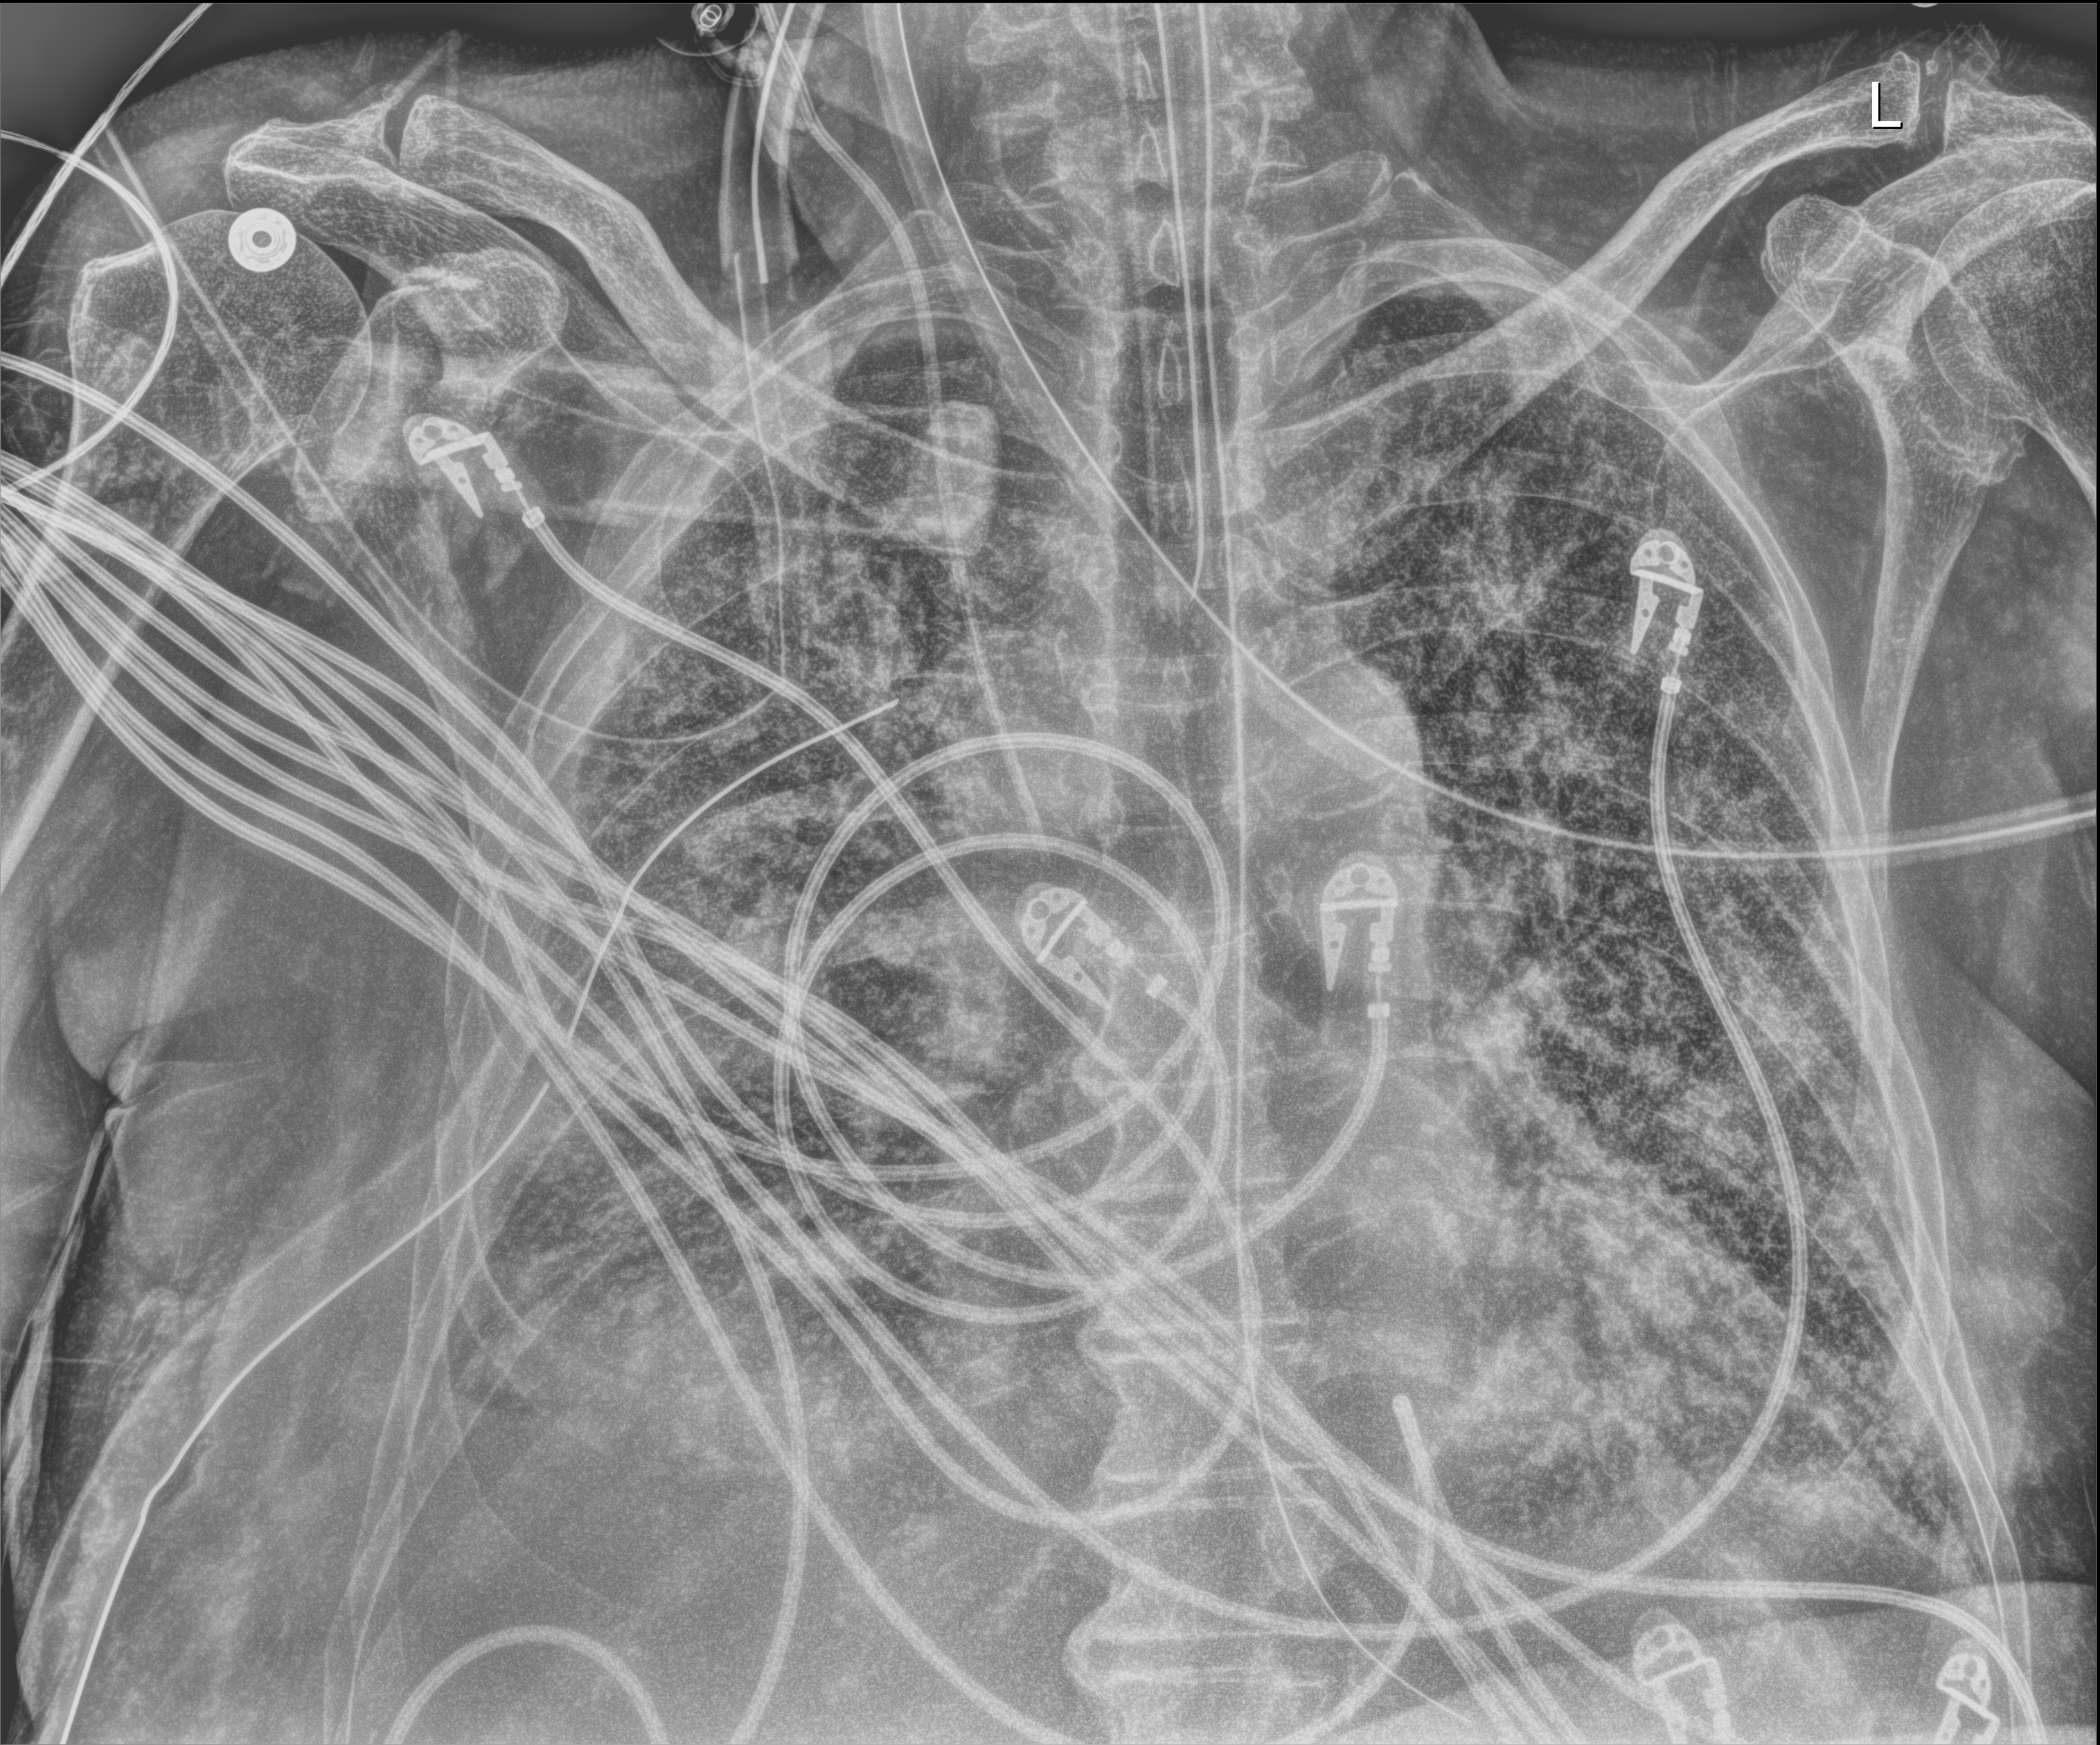
Portable chest radiograph. Patient hospitalised with COVID-19; male, aged 75–90 years.
Hospital-stay facts (about this admission, not read from this image; timing relative to this image not recorded):
- mechanically ventilated during this hospital stay: yes
- admitted to intensive care during this hospital stay: yes